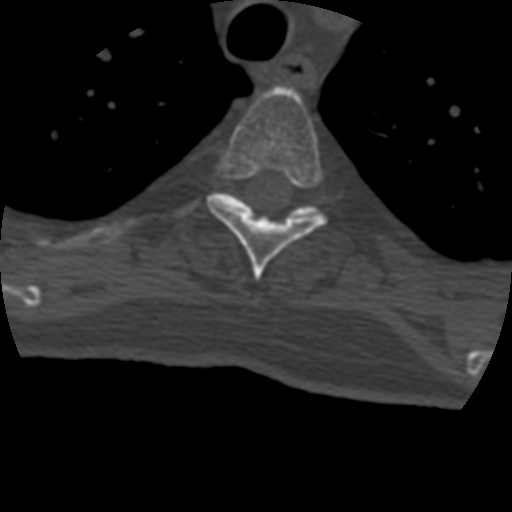
CT including the spine, one axial slice. Slice 334 of 399 in the series (ordered by position). Reconstruction kernel STANDARD. 120 kVp. Bone window (W 1800 / L 400 HU). 1.25 mm slice thickness. 512 × 512 image matrix. Patient age 69 years. Case-level facts recorded for this patient, not image findings: primary cancer: prostate.
Outlined on this slice (semi-automatic segmentation, software-assisted and operator-edited):
- T4 vertebra: bounding box (x1, y1, x2, y2) in pixels: (207, 87, 328, 281)
- T5 vertebra: (183, 193, 321, 238)